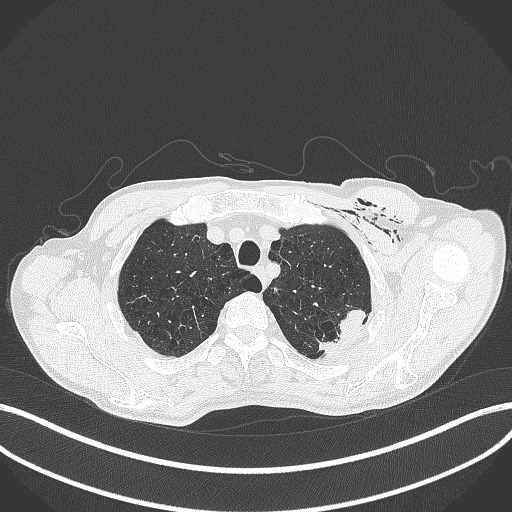
Chest CT, one axial slice. Position 353 of 457 along the scan axis. Reconstruction kernel B70f. Lung window (W 1500 / L -600 HU). 1 mm slice thickness. 512 × 512 image matrix. Male patient, age 58 years. Case-level facts recorded for this patient, not image findings: clinical TNM (as recorded): T3 N0 M0.
Structures marked on this image (rectangle marked by the reading radiologist):
- lung tumour (recorded histology: adenocarcinoma): bounding box (x1, y1, x2, y2) in pixels: (310, 306, 378, 354)